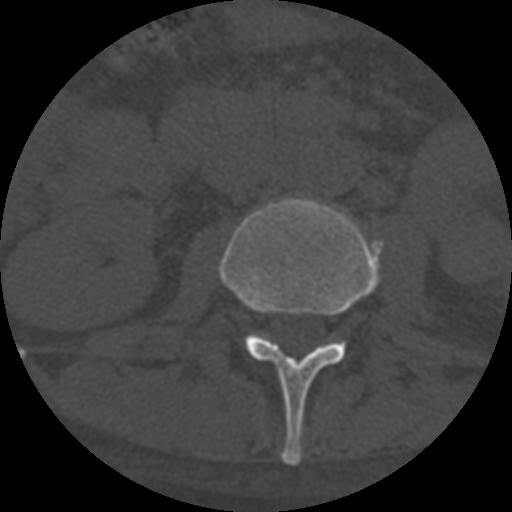
CT including the spine, one axial slice; position 255 of 708 along the scan axis; 120 kVp; one of 3 acquisitions stored at this slice position; bone window (W 1800 / L 400 HU); 1.25 mm slice thickness; 512 × 512 image matrix, field of view 160 × 160 mm. Patient age 55 years. From the clinical record (not read from this slice): primary cancer: colon; vertebrae with lytic lesions (as recorded): T12, L1, L5.
Outlined on this slice (semi-automatically segmented with operator editing):
- L2 vertebra: bounding box <220,197,384,465> (left, top, right, bottom; pixels)